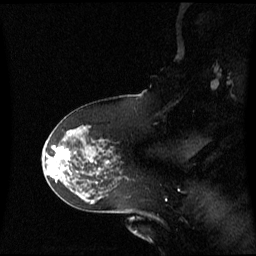
Breast MRI (dynamic contrast-enhanced), one sagittal slice; slice 41 of 60 in the series (ordered by position); dynamic contrast-enhanced series, image 2 of 3 at this slice position (ordered by acquisition); 1.5 T; TE 4.2 ms, TR 8.4 ms; 2.3 mm slice thickness; 256 × 256 image matrix. Female patient, age 60 years. Case-level facts recorded for this patient, not image findings: setting: breast cancer imaged before/during neoadjuvant chemotherapy; receptor status: HR-positive, HER2-negative.
Annotated regions visible in this slice (semi-automatic segmentation, software-assisted and operator-edited):
- analysis volume of interest (the breast-tissue region the enhancement analysis was run in; not a lesion): box from (x=46, y=141) to (x=78, y=171) px
- tumour enhancement mask (voxels above the 70 % enhancement threshold inside the analysis volume of interest): (x=60, y=153)–(x=62, y=155)